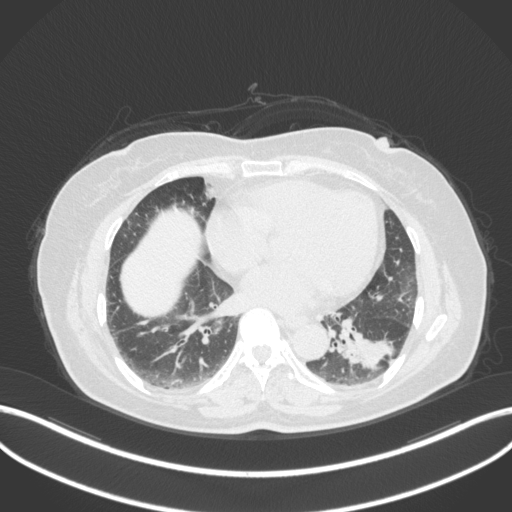
Chest CT, one axial slice; slice 149 of 307 in the series (ordered by position); reconstruction kernel B31f; lung window (W 1500 / L -600 HU); 1 mm slice thickness; 512 × 512 image matrix. Patient: female, 59 years. From the clinical record (not read from this slice): clinical TNM (as recorded): T2a N0 M0; histopathological grade: G2-3.
Structures marked on this image (rectangle marked by the reading radiologist):
- lung tumour (recorded histology: adenocarcinoma): bounding box [x1, y1, x2, y2] px = [330, 315, 398, 375]